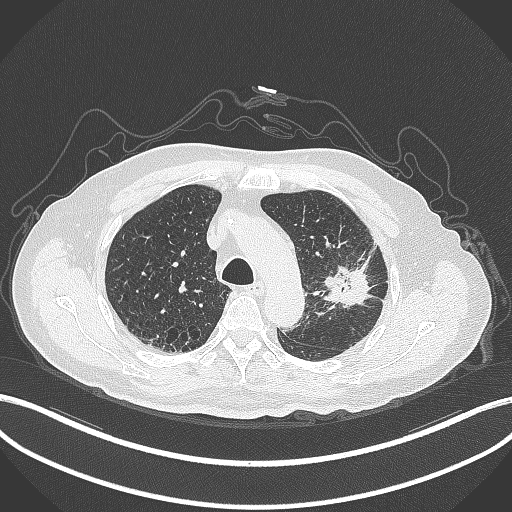
Chest CT, one axial slice; position 219 of 331 along the scan axis; lung window (W 1500 / L -600 HU); 1 mm slice thickness; 512 × 512 image matrix, field of view 400 × 400 mm. Male patient, age 79 years. Case-level facts recorded for this patient, not image findings: clinical TNM (as recorded): T2a N1 M1.
Outlined on this slice (bounding box drawn by a radiologist):
- lung tumour (recorded histology: adenocarcinoma): bounding box [x1, y1, x2, y2] px = [313, 240, 387, 311]